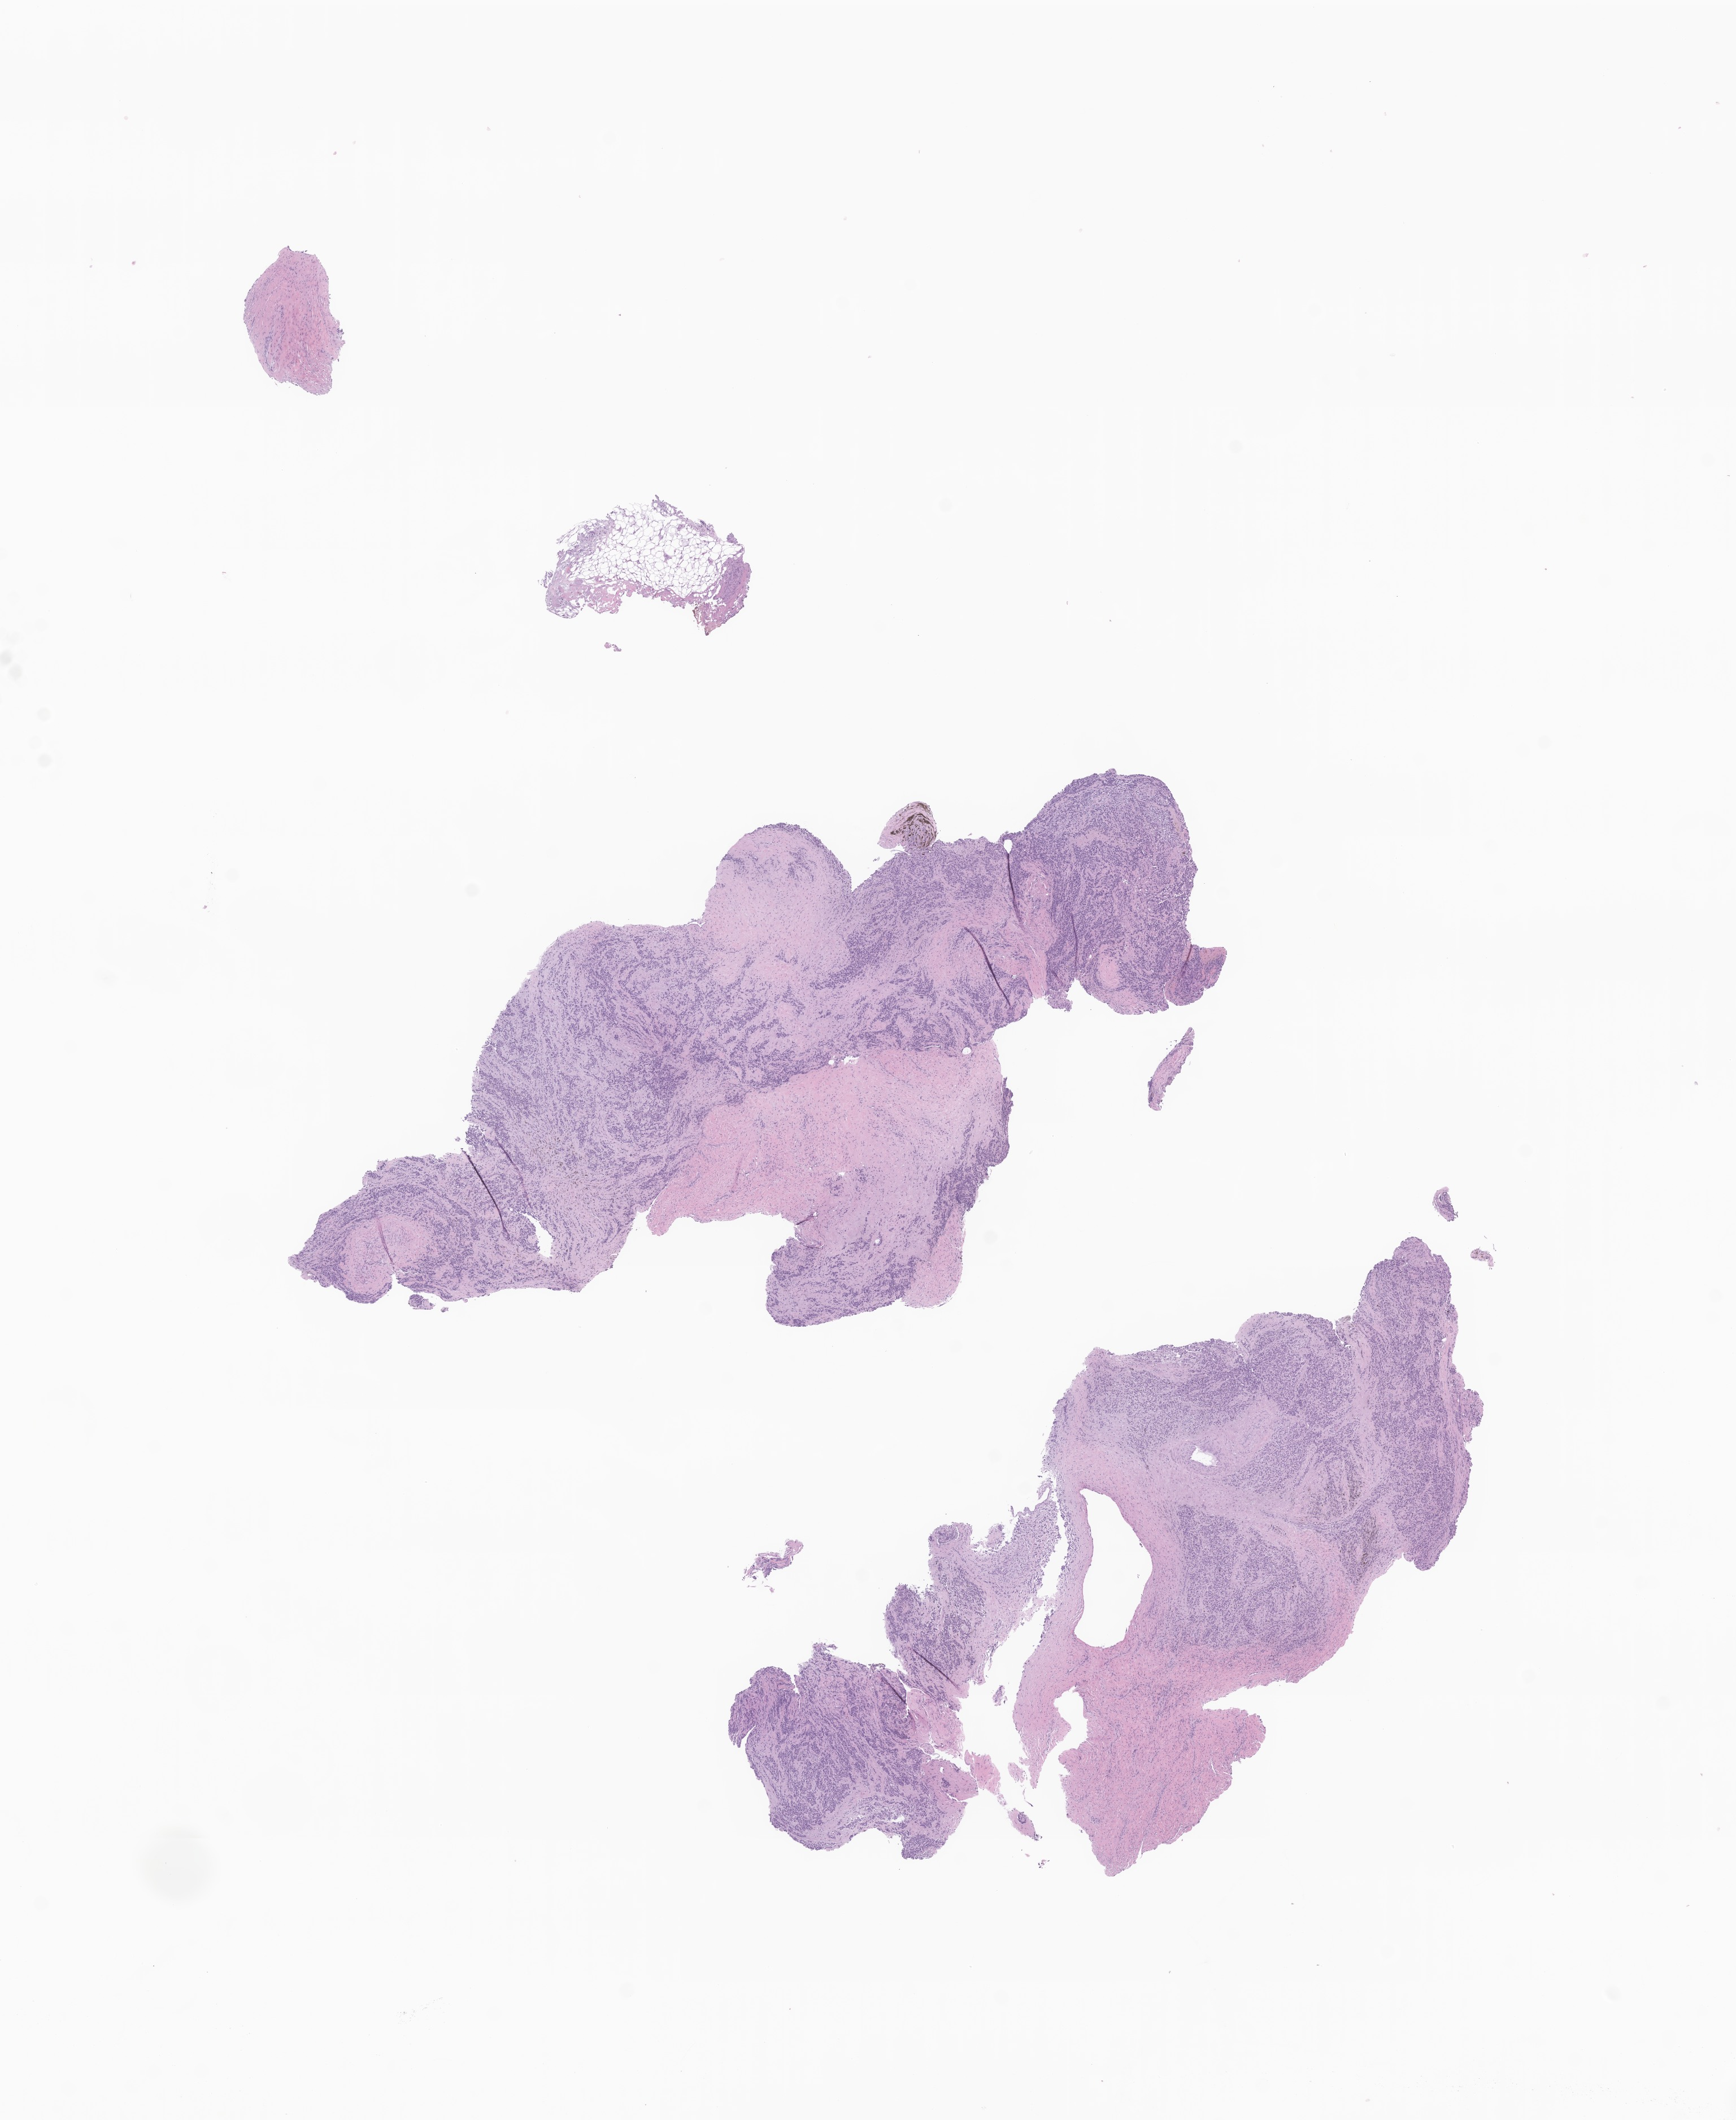
Whole-slide image, haematoxylin and eosin stain of tumor tissue from the soft tissue of lower extremity, shown as a low-resolution overview of the whole scanned area (about 13.0 x 15.8 mm), FFPE section. Female patient, age 185 months (15 years 5 months).
Diagnosis: Clear cell sarcoma, NOS.